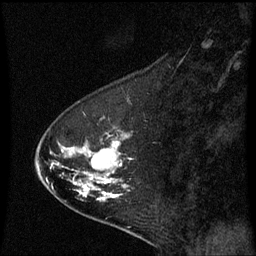
Breast MRI (dynamic contrast-enhanced), one sagittal slice; slice 19 of 60 in the series (ordered by position); dynamic contrast-enhanced series, image 2 of 3 at this slice position (ordered by acquisition); 1.5 T; TE 4.2 ms, TR 8.9 ms; 256 × 256 image matrix, field of view 200 × 200 mm. Patient: female, 53 years. From the clinical record (not read from this slice): setting: breast cancer imaged before/during neoadjuvant chemotherapy; receptor status: HR-positive, HER2-negative.
Outlined on this slice (semi-automatically segmented with operator editing):
- analysis volume of interest (the breast-tissue region the enhancement analysis was run in; not a lesion): bounding box [x1, y1, x2, y2] px = [36, 116, 133, 221]
- tumour enhancement mask (voxels above the 70 % enhancement threshold inside the analysis volume of interest): [82, 142, 125, 197]